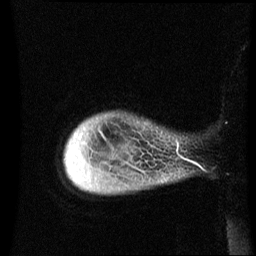
Breast MRI (dynamic contrast-enhanced), one sagittal slice. Slice 3 of 60 in the series (ordered by position). Dynamic contrast-enhanced series, image 2 of 3 at this slice position (ordered by acquisition). 1.5 T. TE 4.2 ms, TR 8.4 ms. 256 × 256 image matrix, field of view 220 × 220 mm. Female patient, age 49 years.
Structures marked on this image (semi-automatically segmented with operator editing):
- analysis volume of interest (the breast-tissue region the enhancement analysis was run in; not a lesion): bounding box (x1, y1, x2, y2) in pixels: (65, 114, 185, 195)
- tumour enhancement mask (voxels above the 70 % enhancement threshold inside the analysis volume of interest): (178, 146, 180, 149)